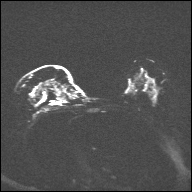
Breast MRI, one axial slice. Position 22 of 32 along the scan axis. Diffusion-weighted series; image 2 of 4 stored at this slice position (different b-values; order by instance number). 1.5 T. 4 mm slice thickness. 192 × 192 image matrix, field of view 360 × 360 mm. Female patient.
Annotated regions visible in this slice (manually delineated by an expert):
- tumour on diffusion-weighted imaging: bounding box <35,79,60,101> (left, top, right, bottom; pixels)